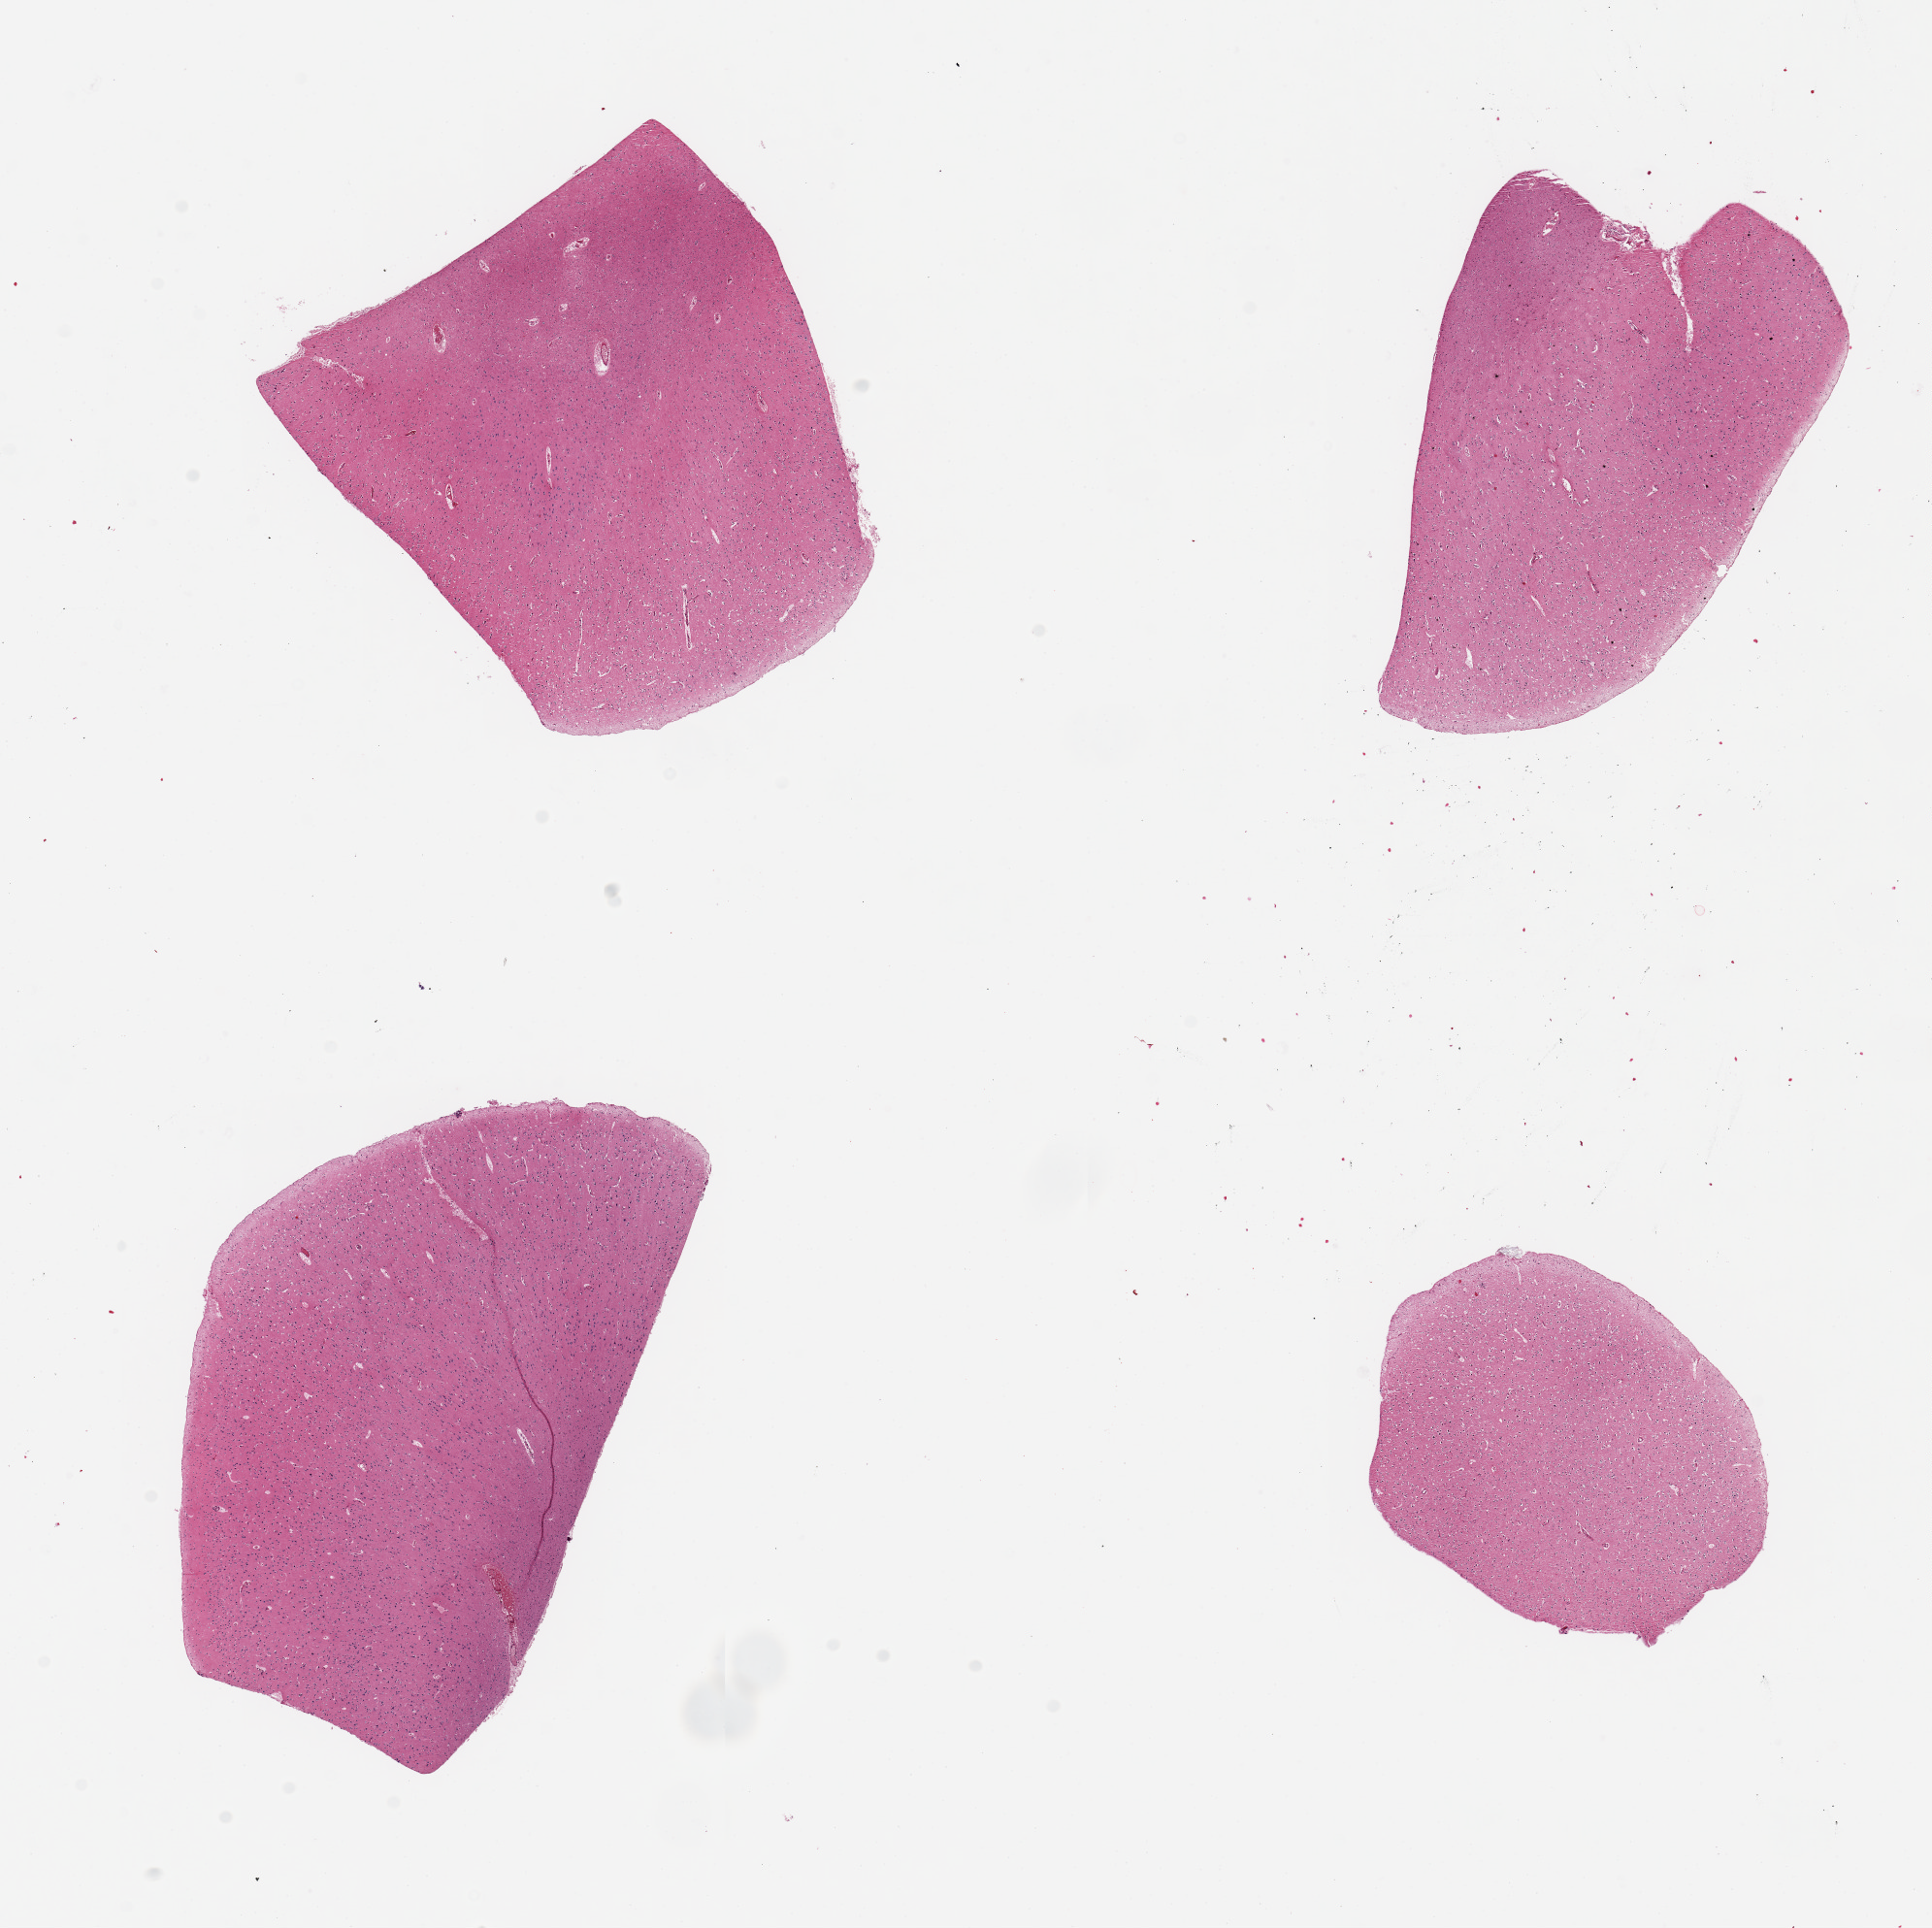
Digitized H&E-stained section, shown as a low-resolution overview of the whole scanned area (about 15.8 x 15.7 mm, acquisition: 20x scan); PAXgene-fixed paraffin-embedded (PFPE) section; section of cerebral cortex (target tissue); donor tissue sample. Donor sex: male.
- pathologist's review note for this sample: 4 pieces, up to 6x4mm